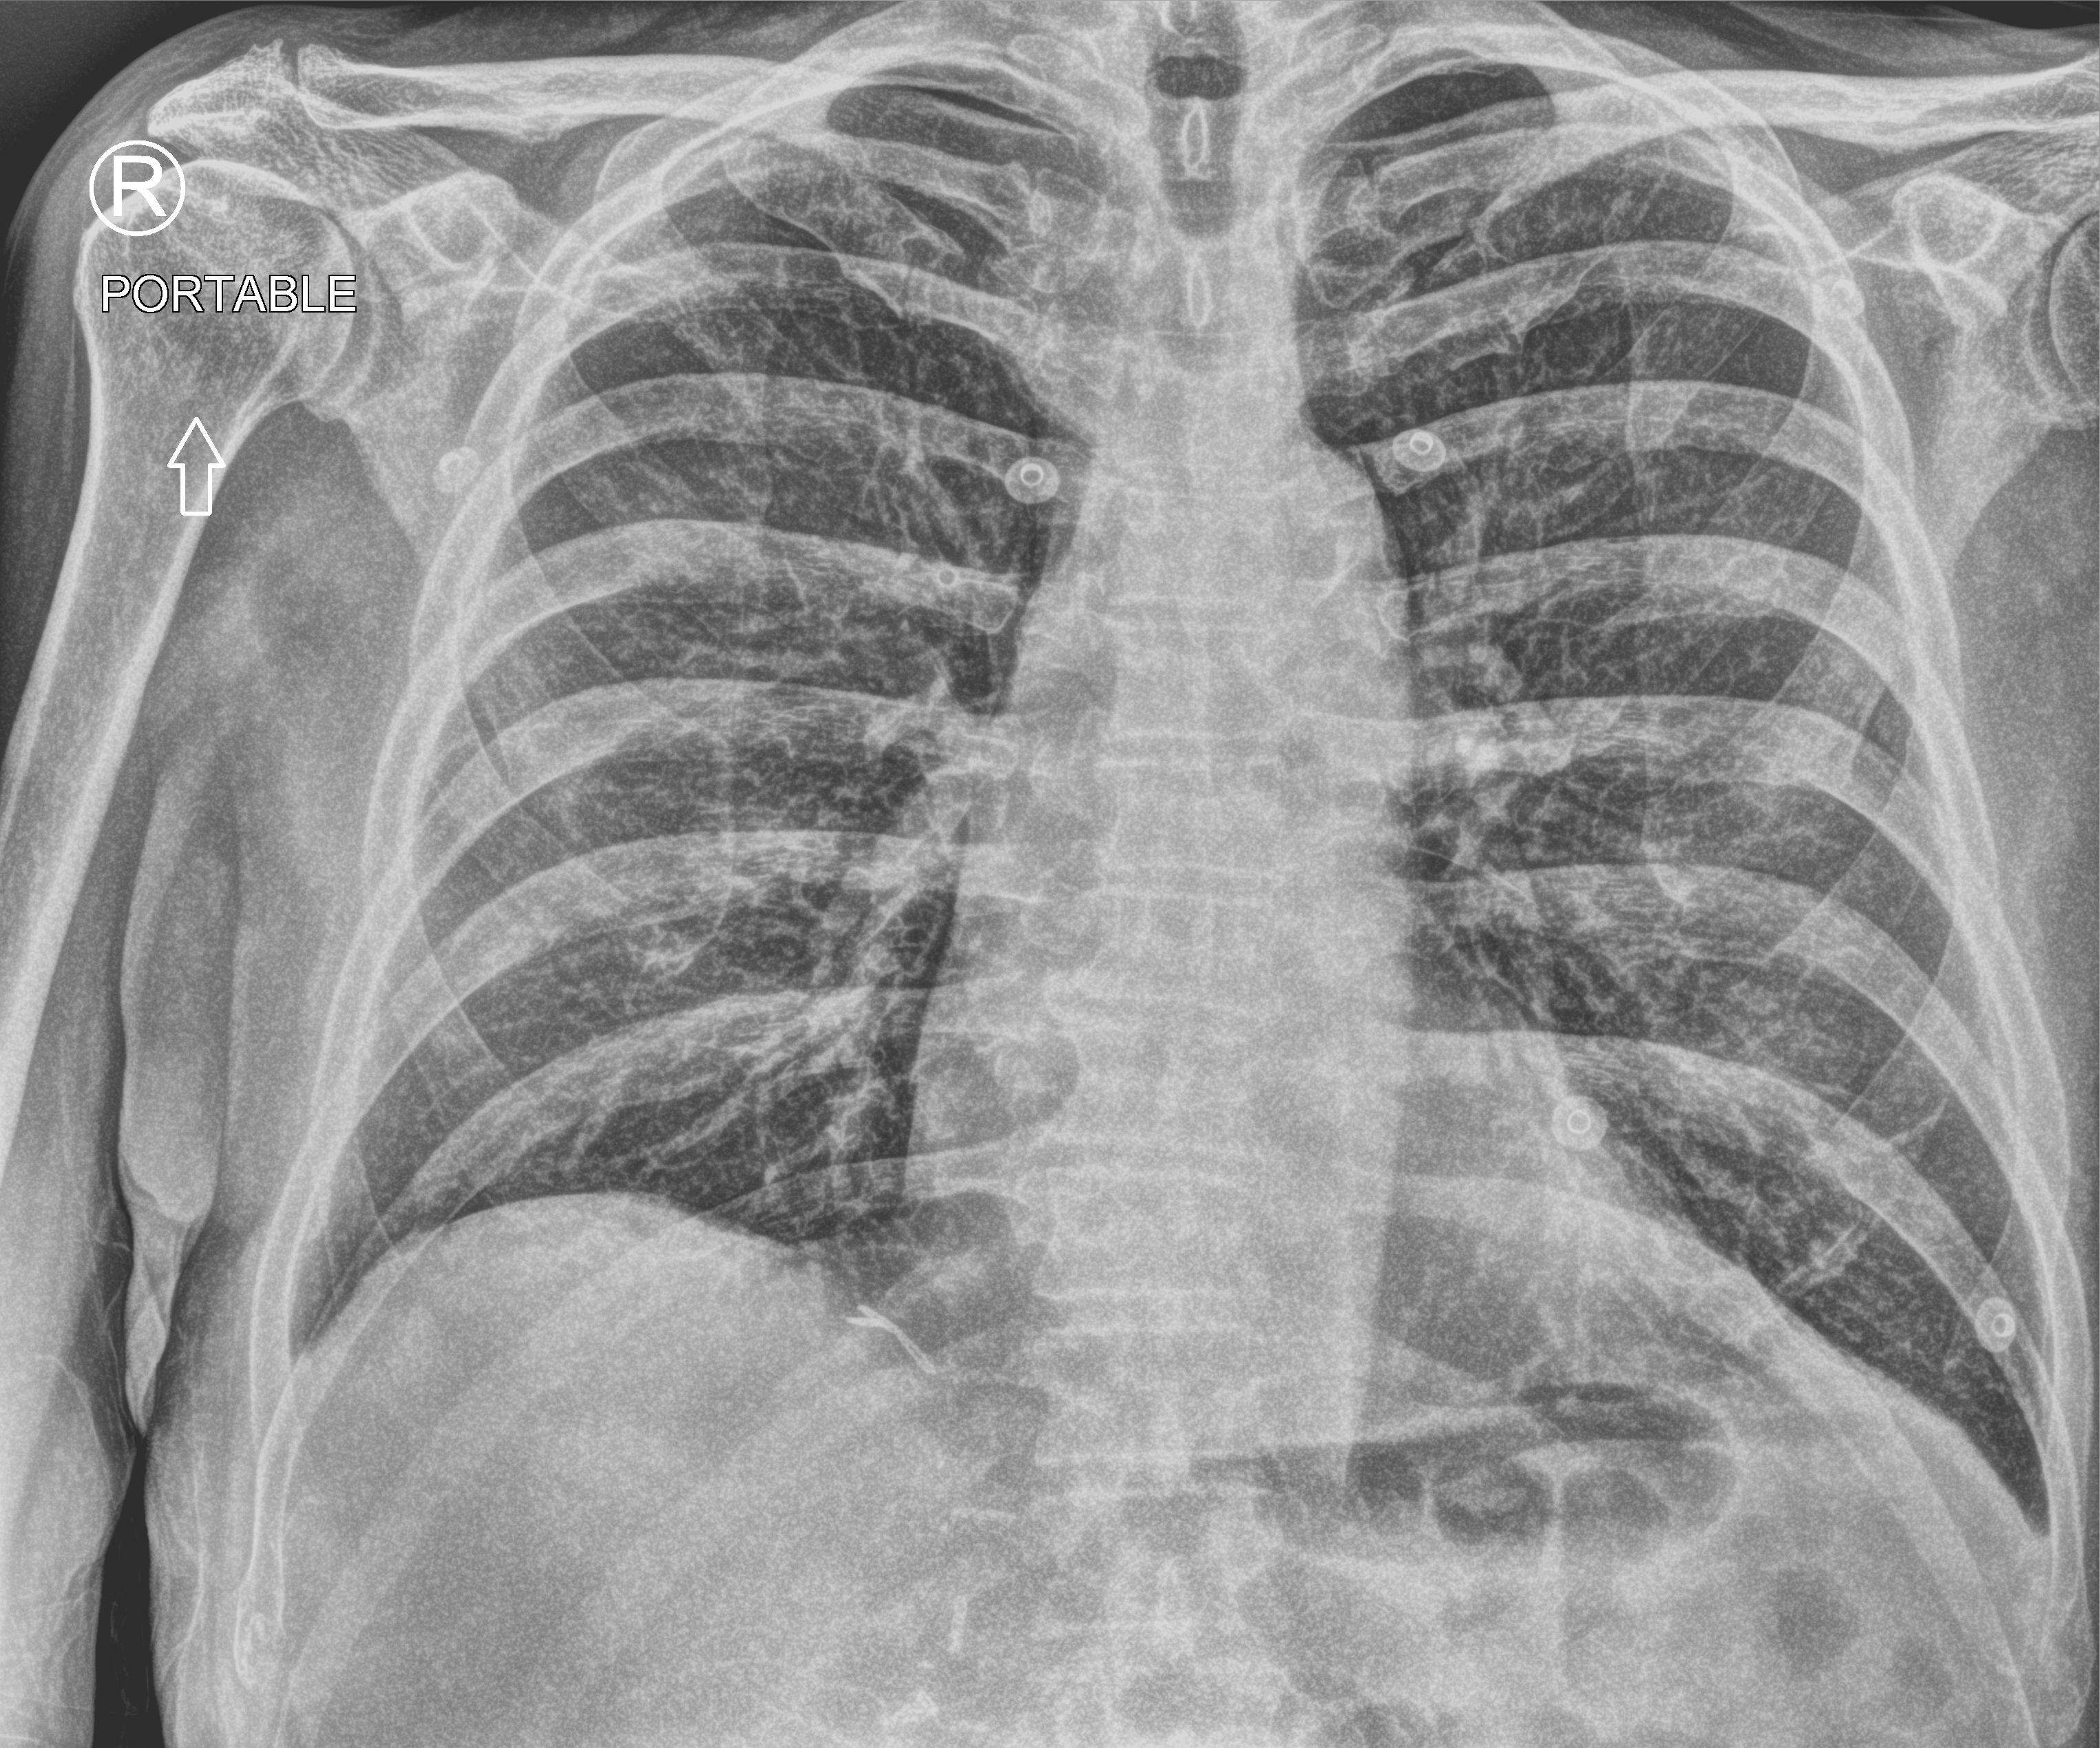
Bedside chest radiograph (computed radiography), anteroposterior (AP) projection. Patient hospitalised with COVID-19; male, aged 60–74 years.
Admission-level facts for this patient (not findings on this image; timing relative to this image not recorded): mechanically ventilated during this hospital stay: no.